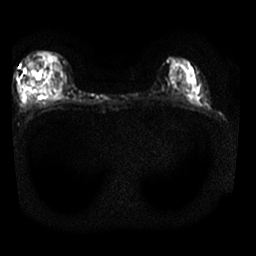
Breast MRI, one axial slice; position 12 of 25 along the scan axis; diffusion-weighted series; image 2 of 4 stored at this slice position (different b-values; order by instance number); 1.5 T; 256 × 256 image matrix, field of view 310 × 310 mm. Female patient.
Annotated regions visible in this slice (manually delineated by an expert):
- tumour on diffusion-weighted imaging: bounding box (x1, y1, x2, y2) in pixels: (44, 87, 47, 92)